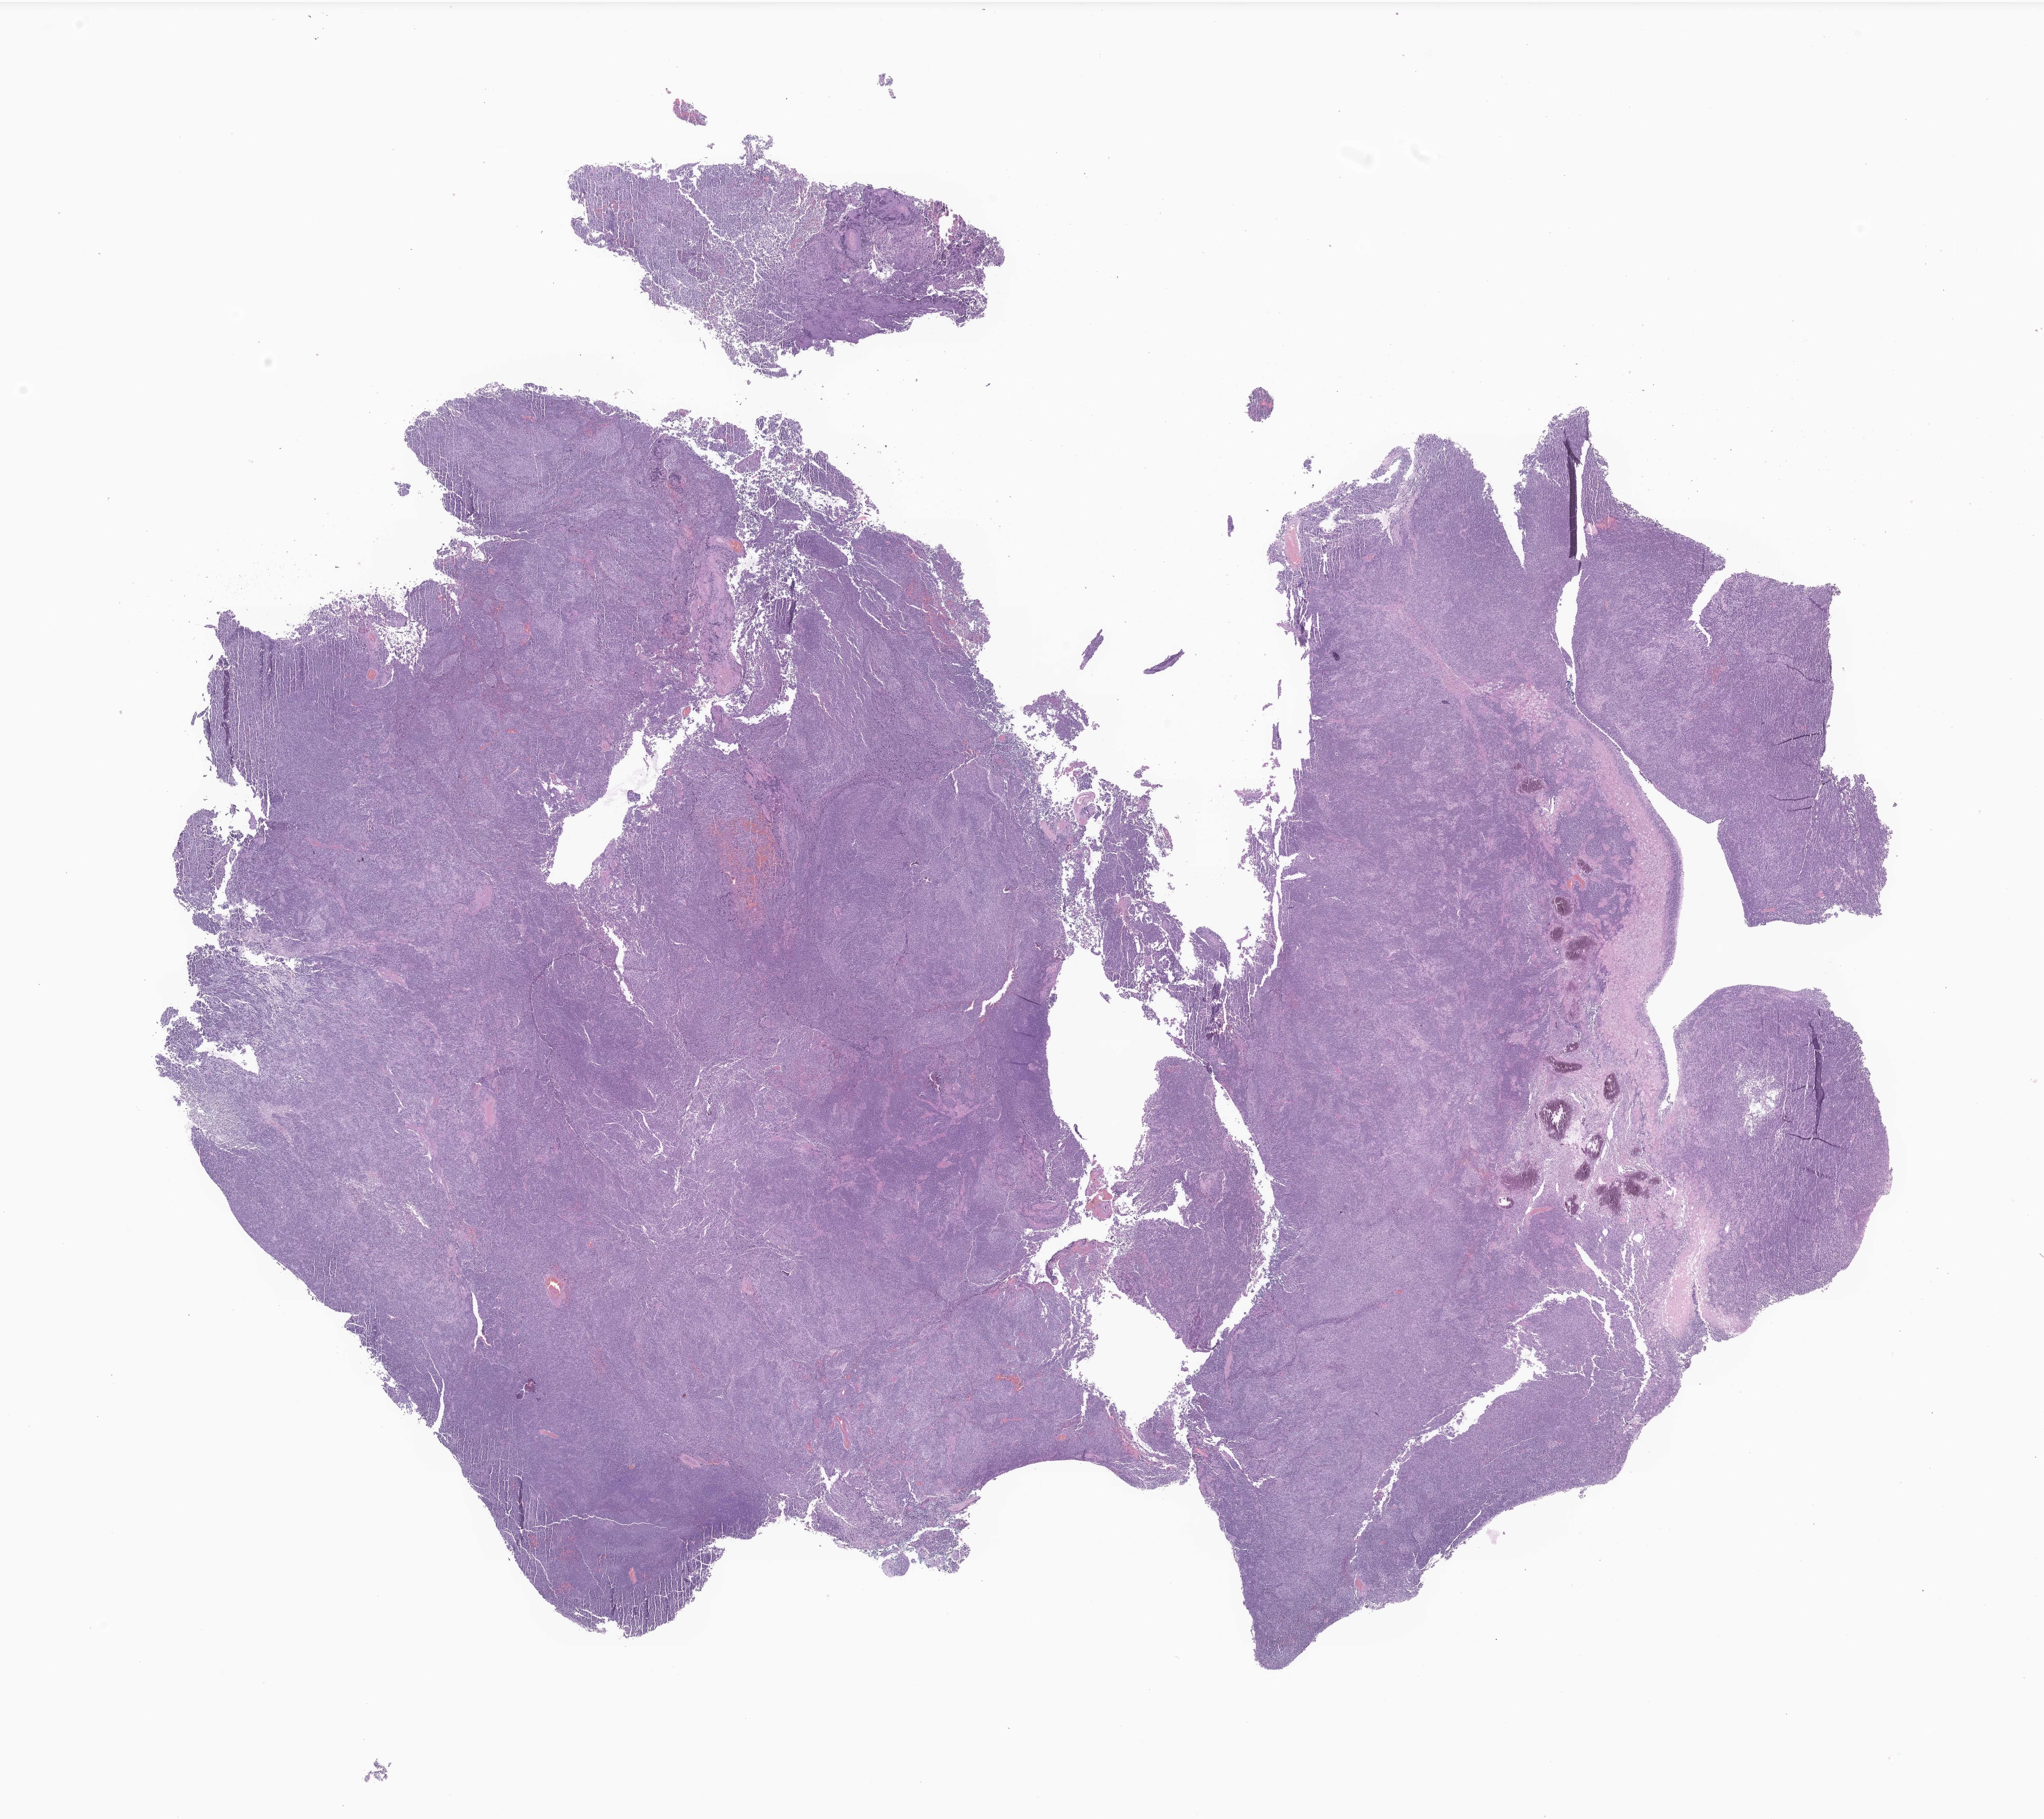
Digitized H&E-stained section of tumor tissue from the brain, whole scanned area (about 25.1 x 22.4 mm) shown as a low-resolution overview; formalin-fixed paraffin-embedded section. Female patient, age 80 months (6 years 8 months).
Diagnosis: Medulloblastoma, NOS.